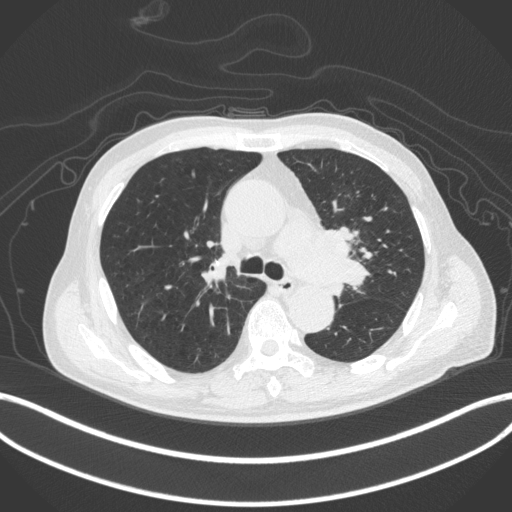
Chest CT, one axial slice; position 284 of 420 along the scan axis; reconstruction kernel B31f; 120 kVp; lung window (W 1500 / L -600 HU); 1 mm slice thickness; 512 × 512 image matrix, field of view 400 × 400 mm. Patient: male, 77 years. From the clinical record (not read from this slice): clinical TNM (as recorded): T3 N1 M0.
Structures marked on this image (rectangle marked by the reading radiologist):
- lung tumour (recorded histology: adenocarcinoma): bounding box [x1, y1, x2, y2] px = [302, 223, 371, 300]